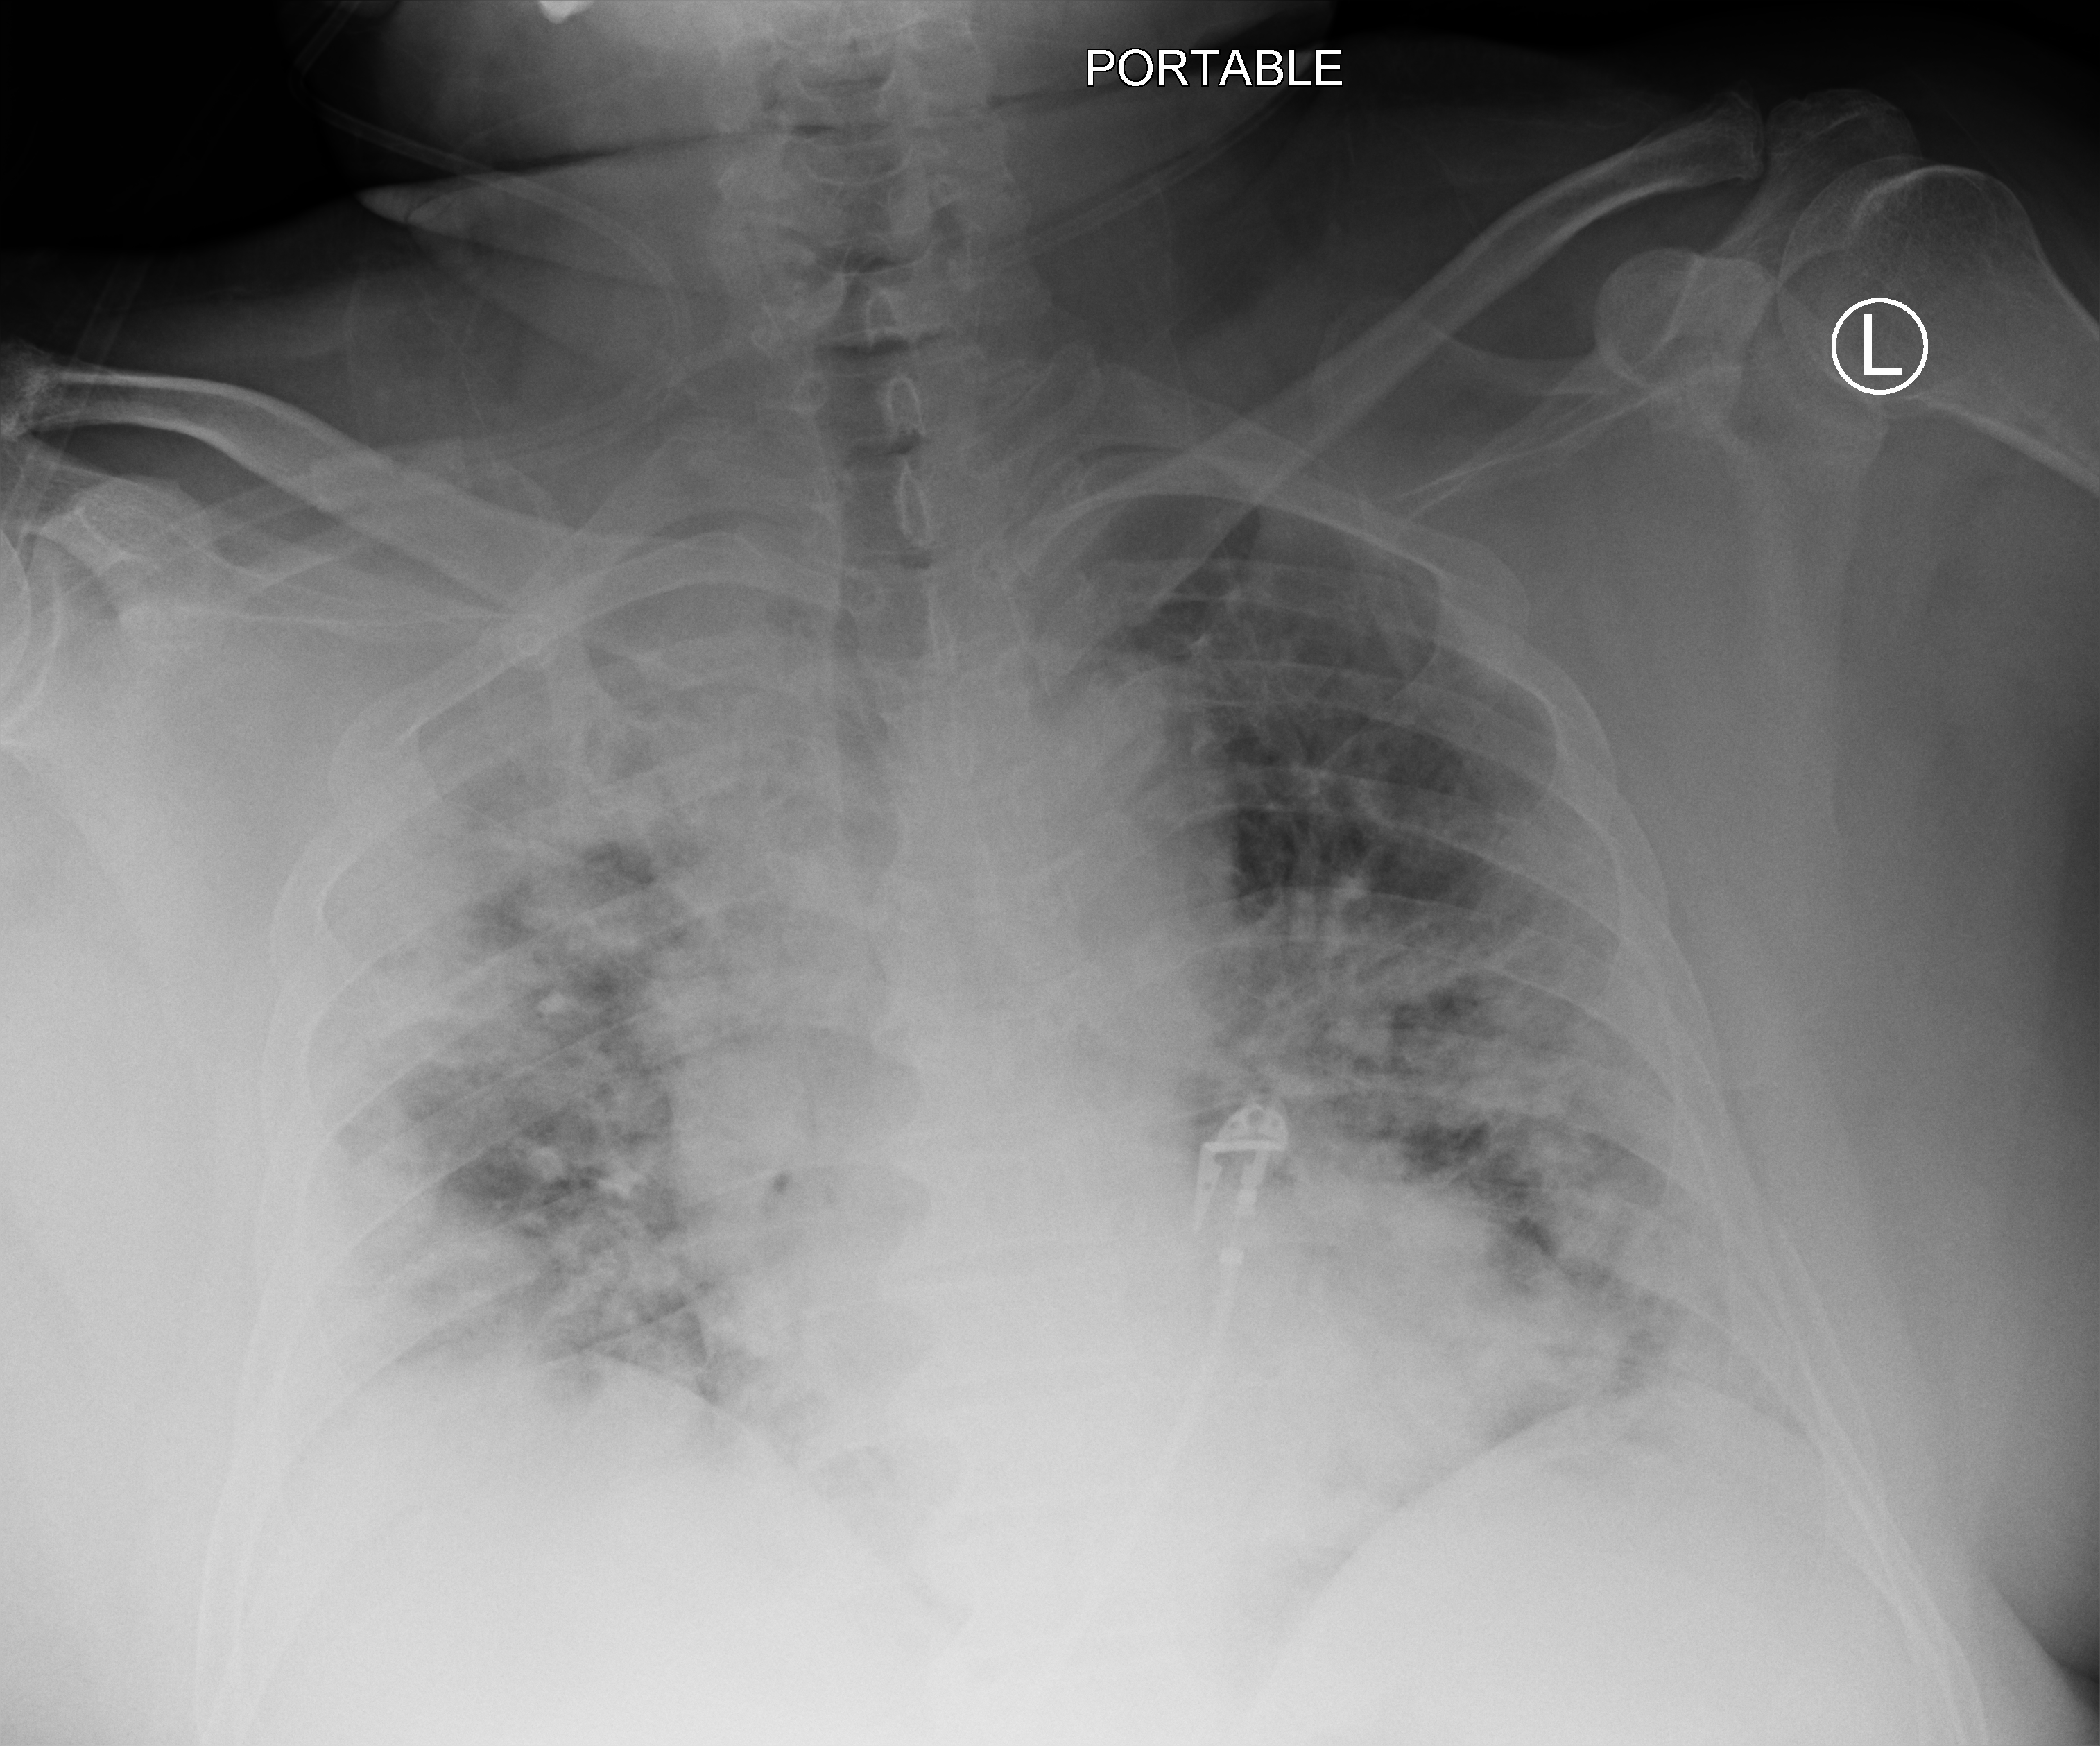
Bedside chest radiograph (computed radiography); anteroposterior (AP) projection. Patient hospitalised with COVID-19, aged 18–59 years.
From the hospital-stay record, not from the radiograph (when in the stay this image was taken is not recorded): length of hospital stay: 28 days; chronic kidney disease (admission record): no; admitted to intensive care during this hospital stay: yes.